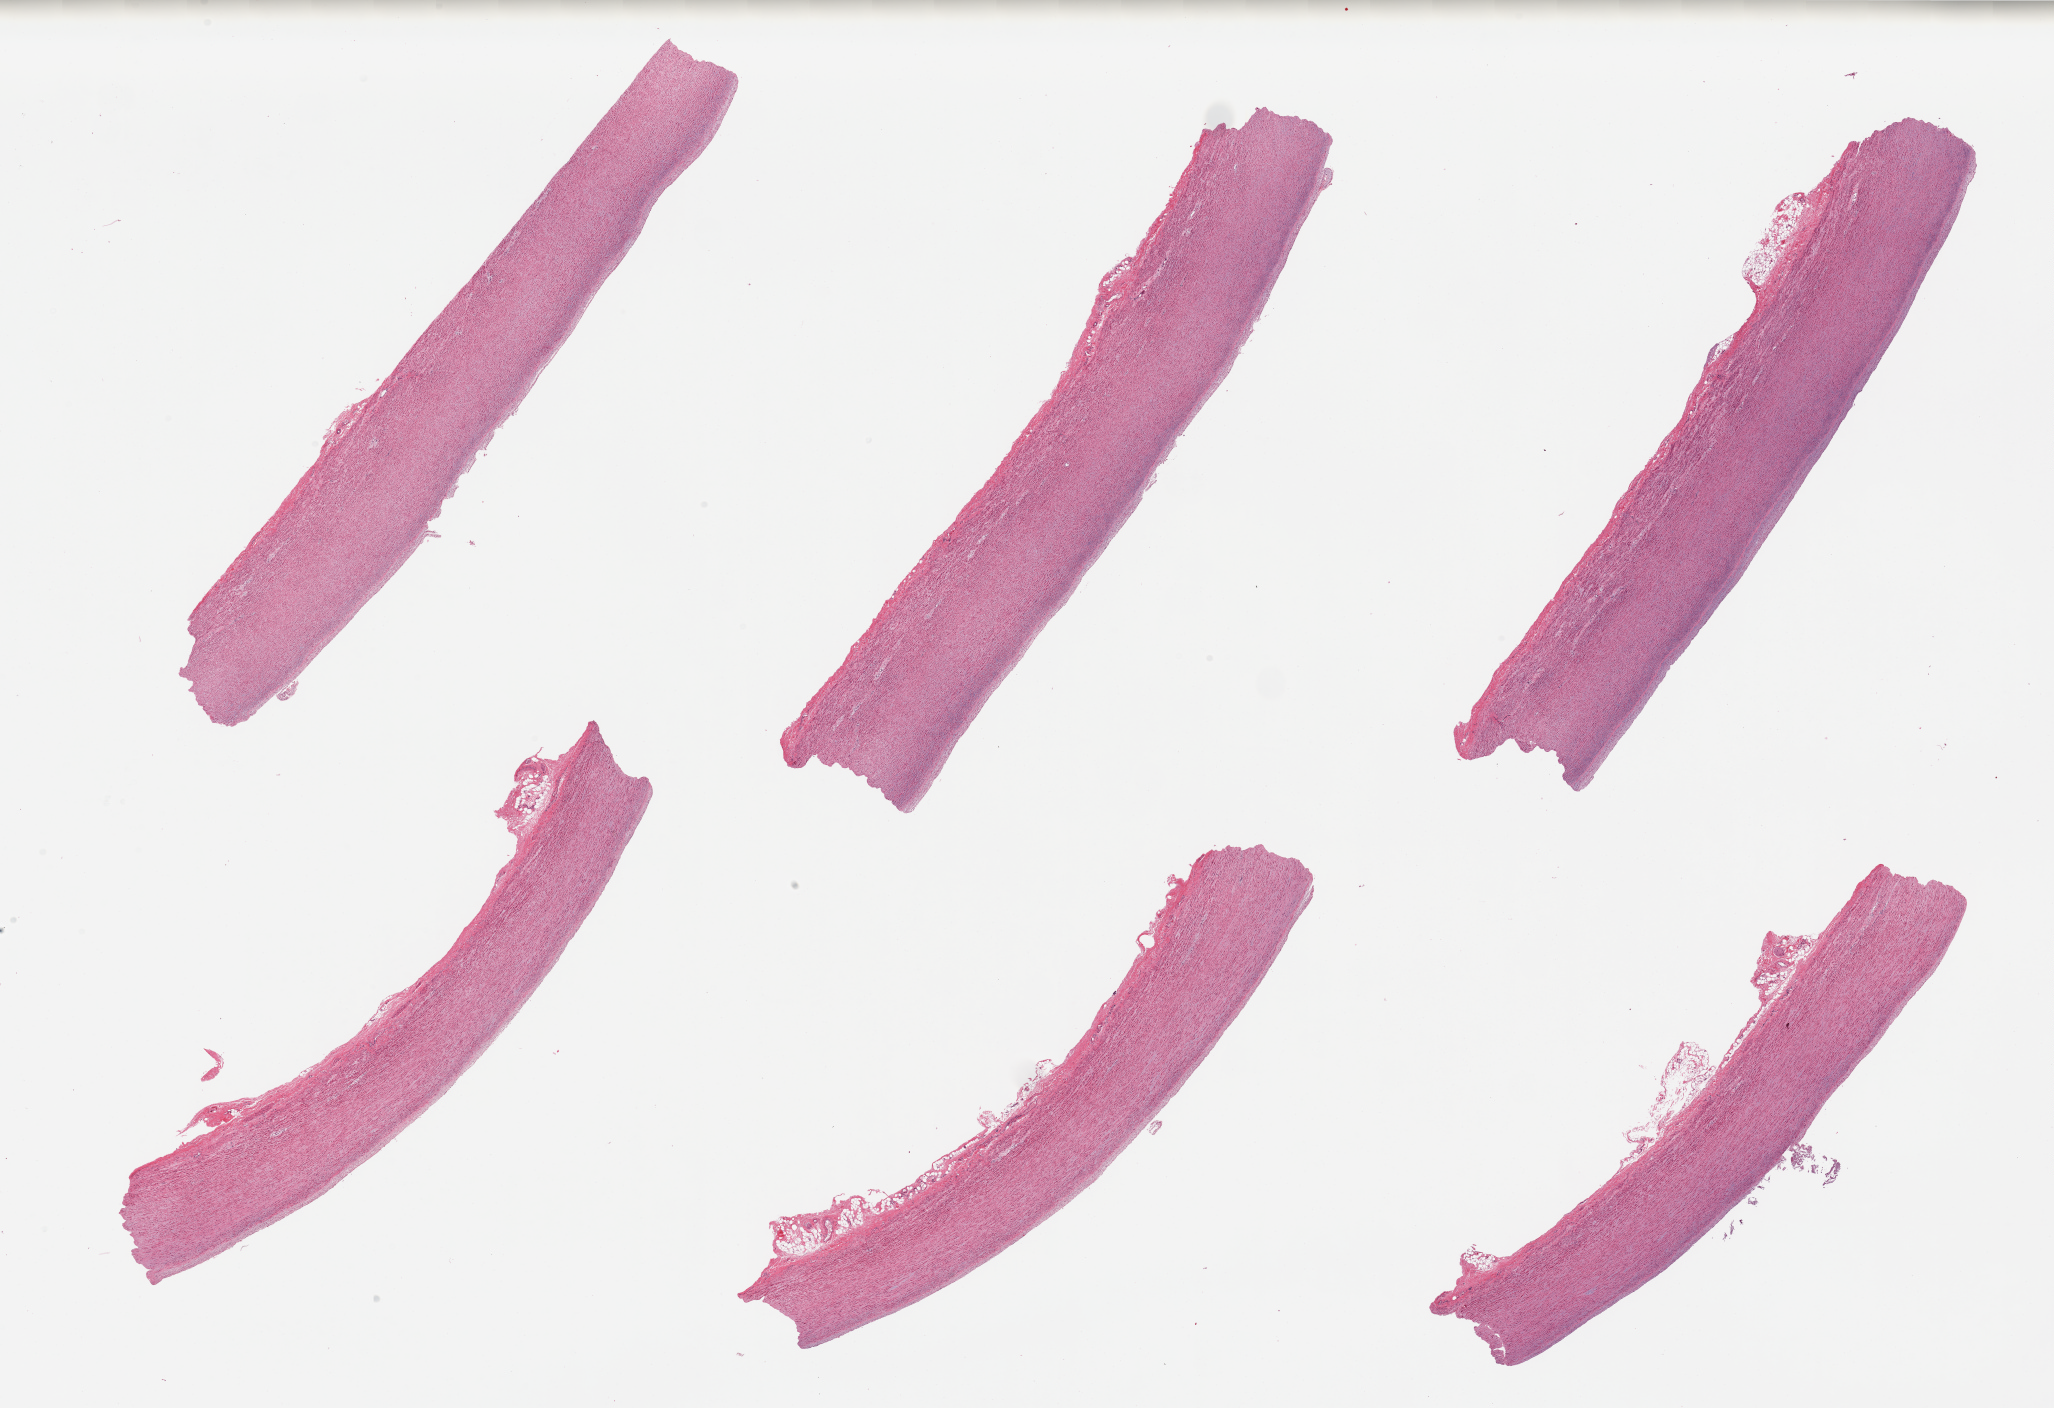
Hematoxylin and eosin (H&E) whole-slide image, shown as a low-resolution overview of the whole scanned area (about 32.5 x 22.3 mm), PAXgene-fixed paraffin-embedded (PFPE) section, section of aorta (target tissue), tissue donor sample. Female donor.
Review note (as recorded): 6 pieces, well trimmed; no plaques.